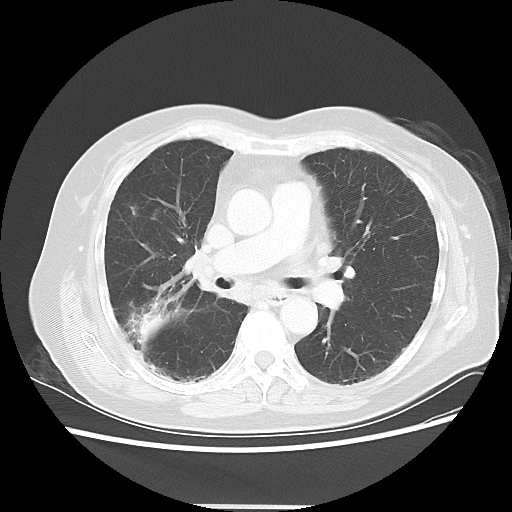
Chest CT, one axial slice. Slice 27 of 50 in the series (ordered by position). Reconstruction kernel LUNG. Lung window (W 1500 / L -600 HU). 512 × 512 image matrix, field of view 360 × 360 mm. Female patient, age 72 years. Case-level facts recorded for this patient, not image findings: clinical TNM (as recorded): T2 N1 M0; histopathological grade: G1.
Annotated regions visible in this slice (bounding box drawn by a radiologist):
- lung tumour (recorded histology: adenocarcinoma): bounding box <135,310,171,346> (left, top, right, bottom; pixels)